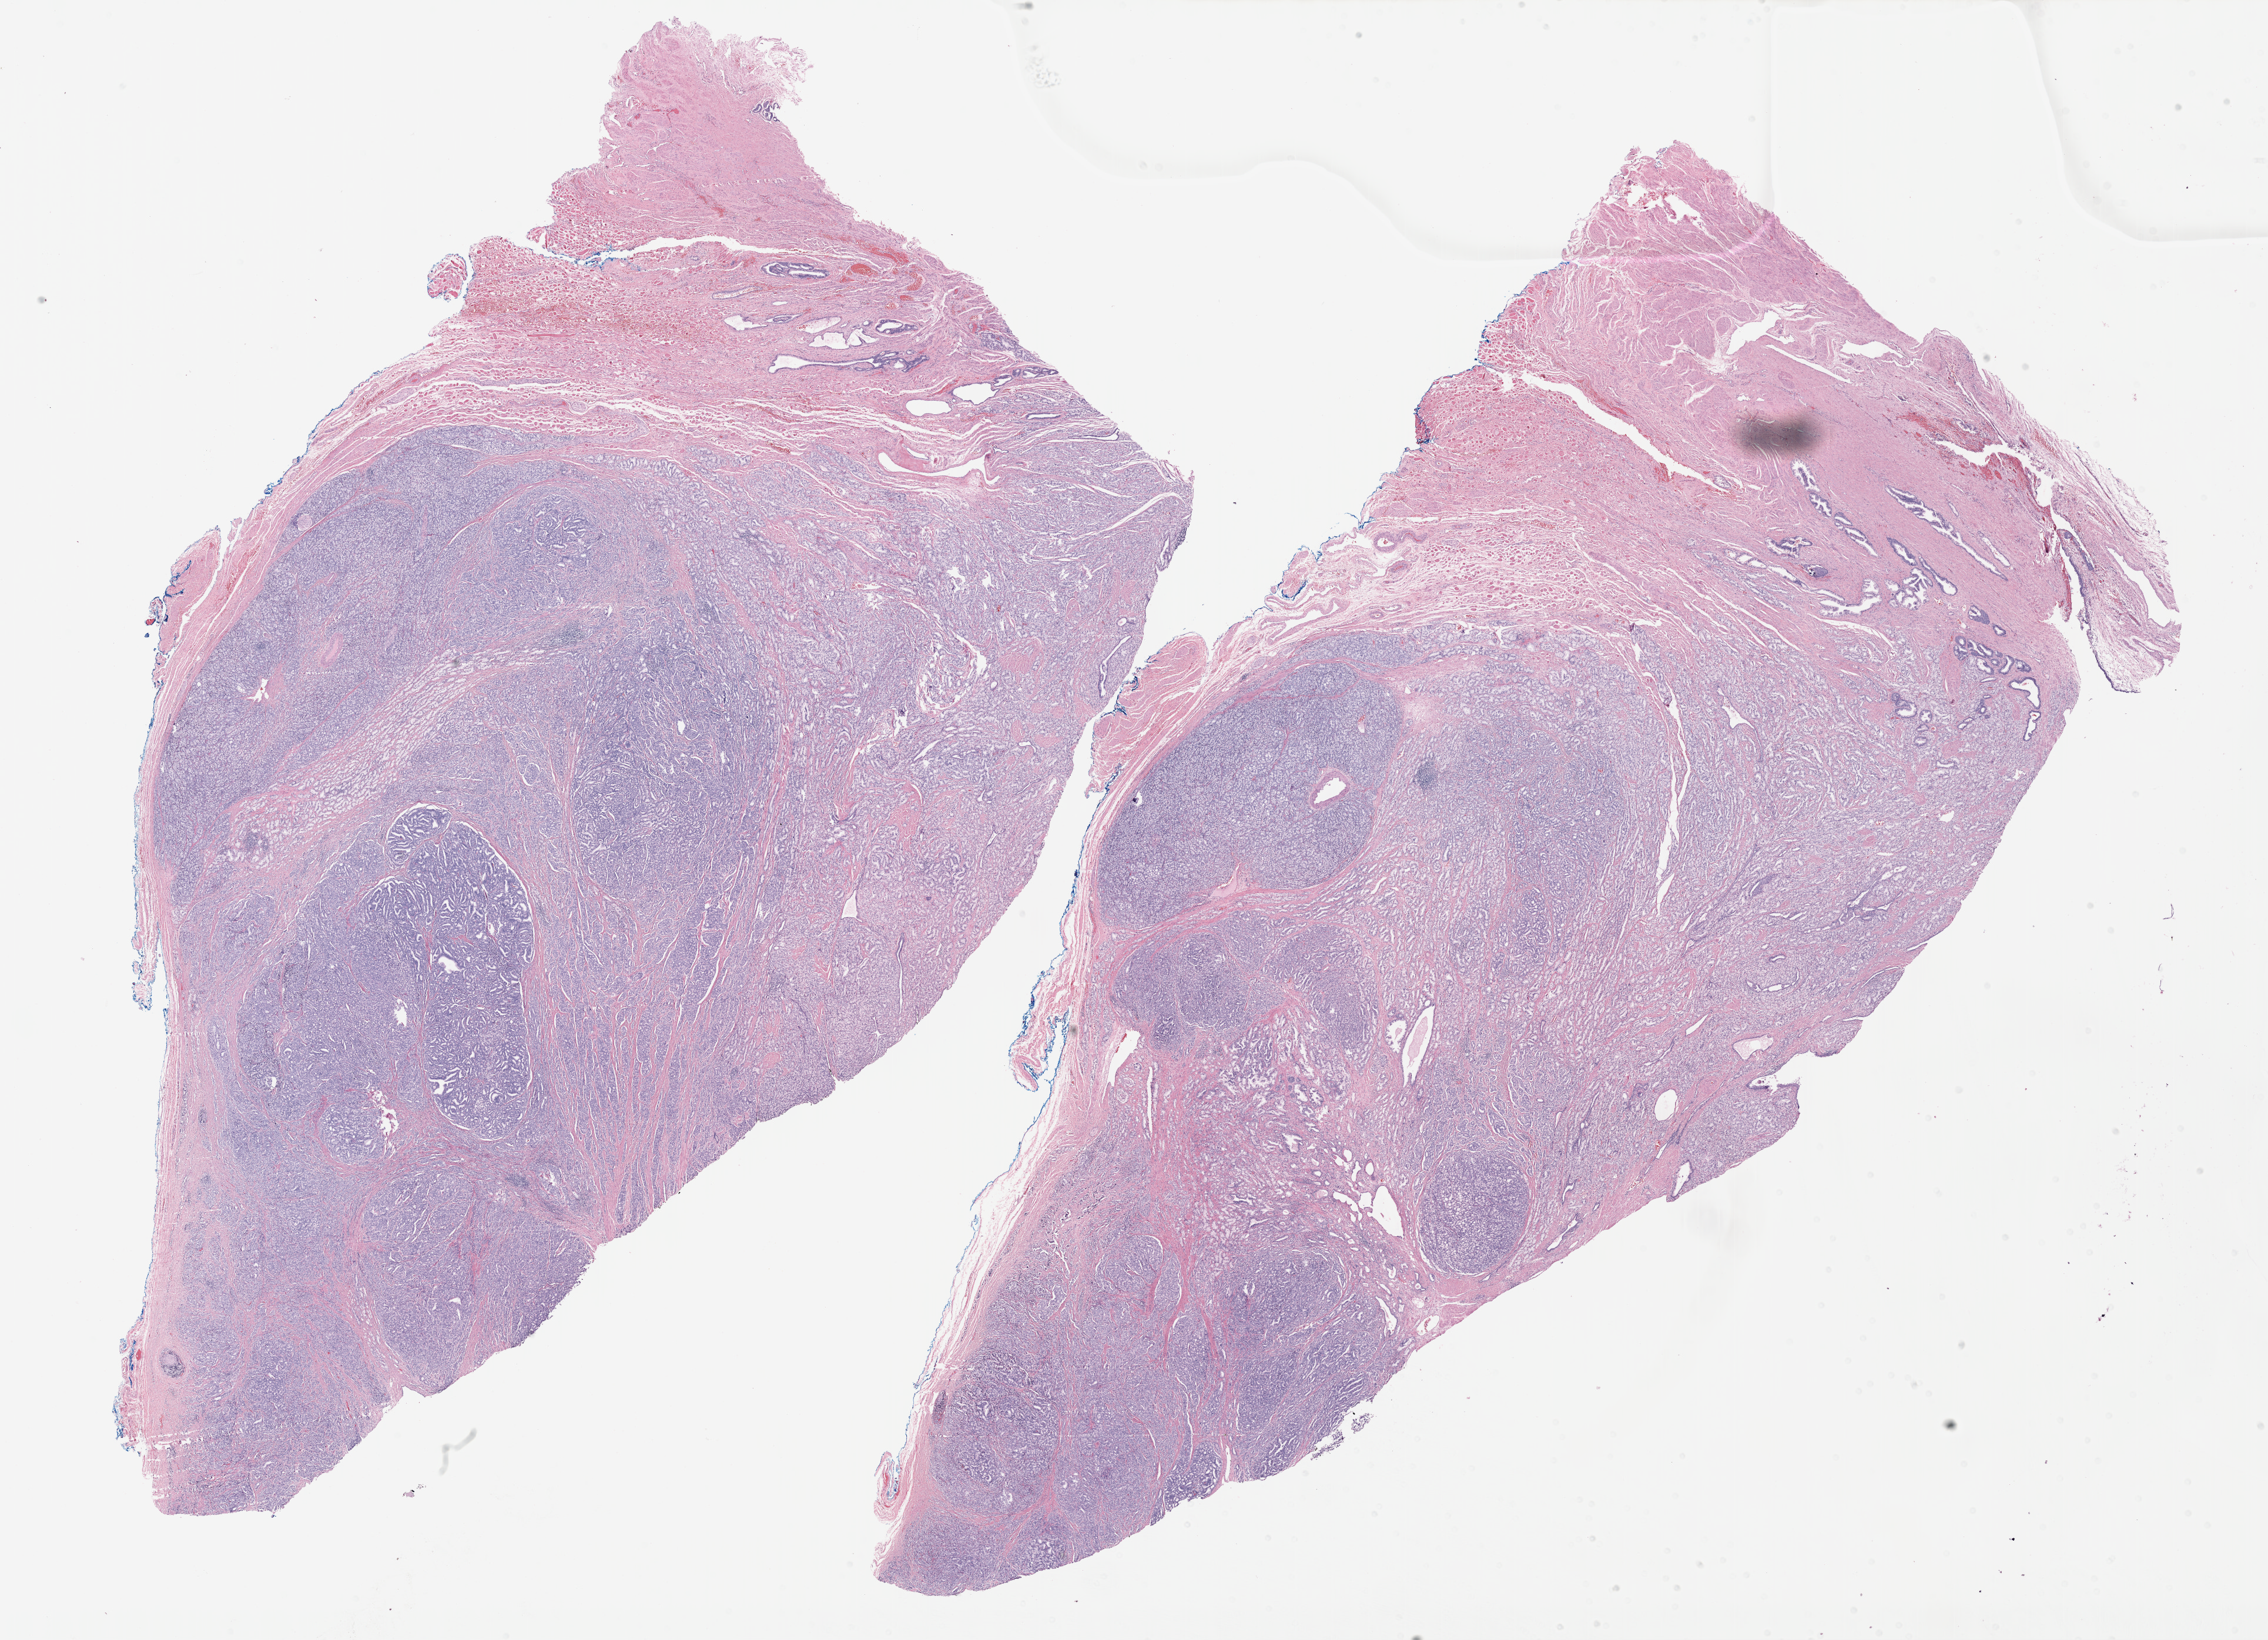
Digitized H&E-stained tissue section (whole slide) — a low-resolution overview of the entire scanned area, about 31.2 x 22.6 mm (from a 40x scan). Formalin-fixed paraffin-embedded (FFPE) diagnostic section. Primary tumour sample from the prostate. Male patient; age at initial diagnosis 70 years.
Histologic diagnosis: Adenocarcinoma, NOS (prostate gland).